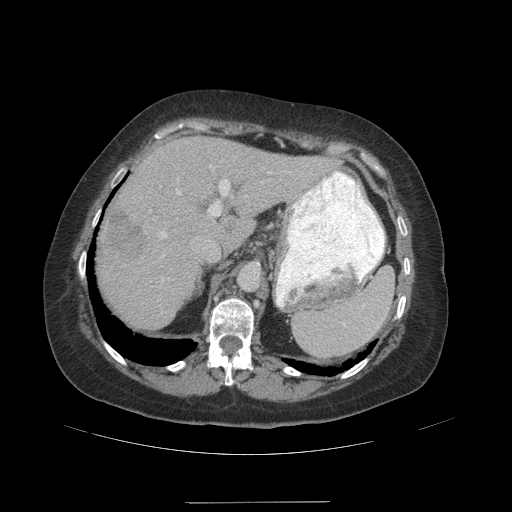
Contrast-enhanced abdominal CT (liver protocol), one axial slice. Position 70 of 99 along the scan axis. Reconstruction kernel STANDARD. Soft-tissue window (W 400 / L 40 HU). 512 × 512 image matrix, field of view 440 × 440 mm. Case-level facts recorded for this patient, not image findings: diagnosis: hepatocellular carcinoma (patient treated with transarterial chemoembolisation; whether this scan precedes or follows treatment is not stated here); TNM stage (as recorded): Stage-IVA; Child-Pugh class: A.
Structures marked on this image (semi-automatic segmentation, software-assisted and operator-edited):
- liver parenchyma outside the tumour (the mass and vessels are separate outlines, so this box may not span the whole liver): bounding box [x1, y1, x2, y2] px = [96, 136, 330, 328]
- mass: [103, 210, 146, 261]
- liver vessels: [160, 165, 270, 238]